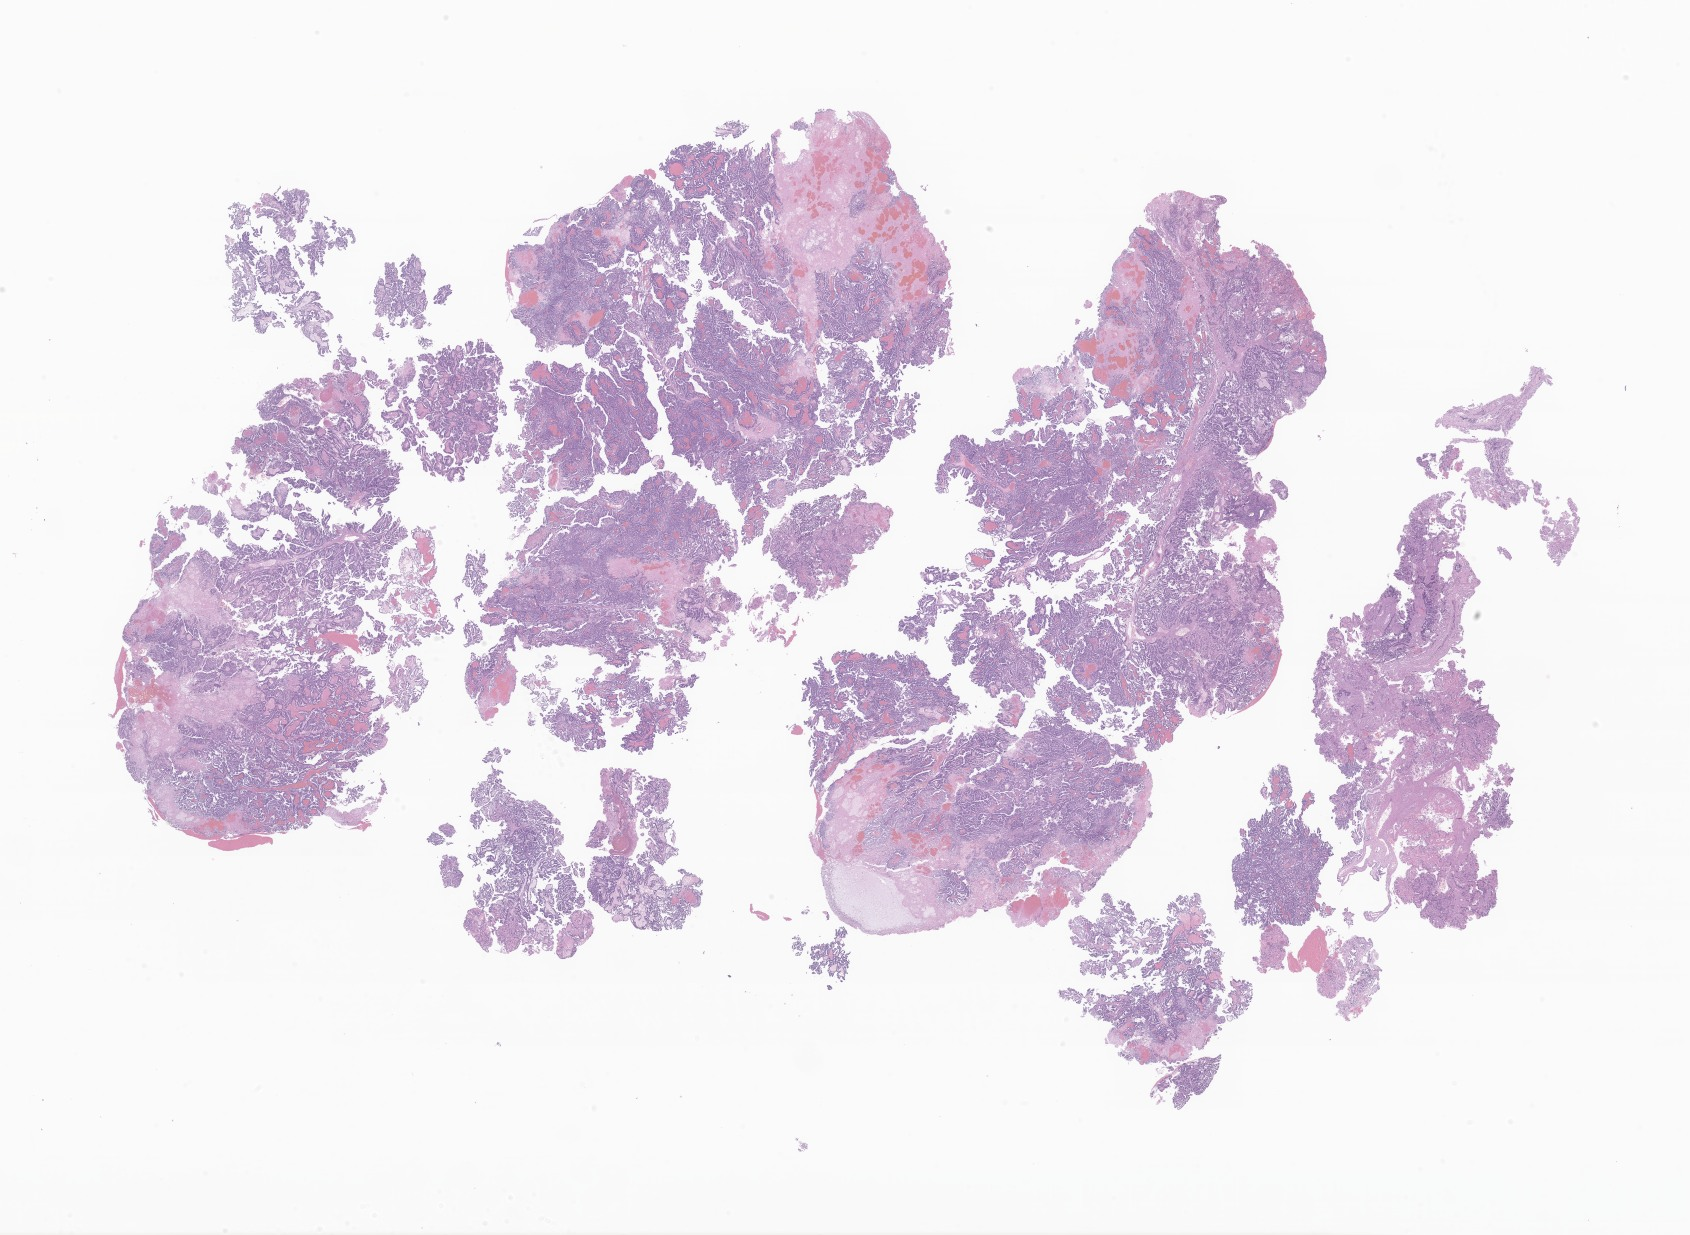
Hematoxylin and eosin (H&E) whole-slide image of tumor tissue from the brain, shown as a low-resolution overview of the whole scanned area (about 28.5 x 20.8 mm); formalin-fixed paraffin-embedded section. Patient male; age 190 days.
Recorded diagnosis: Atypical choroid plexus papilloma.